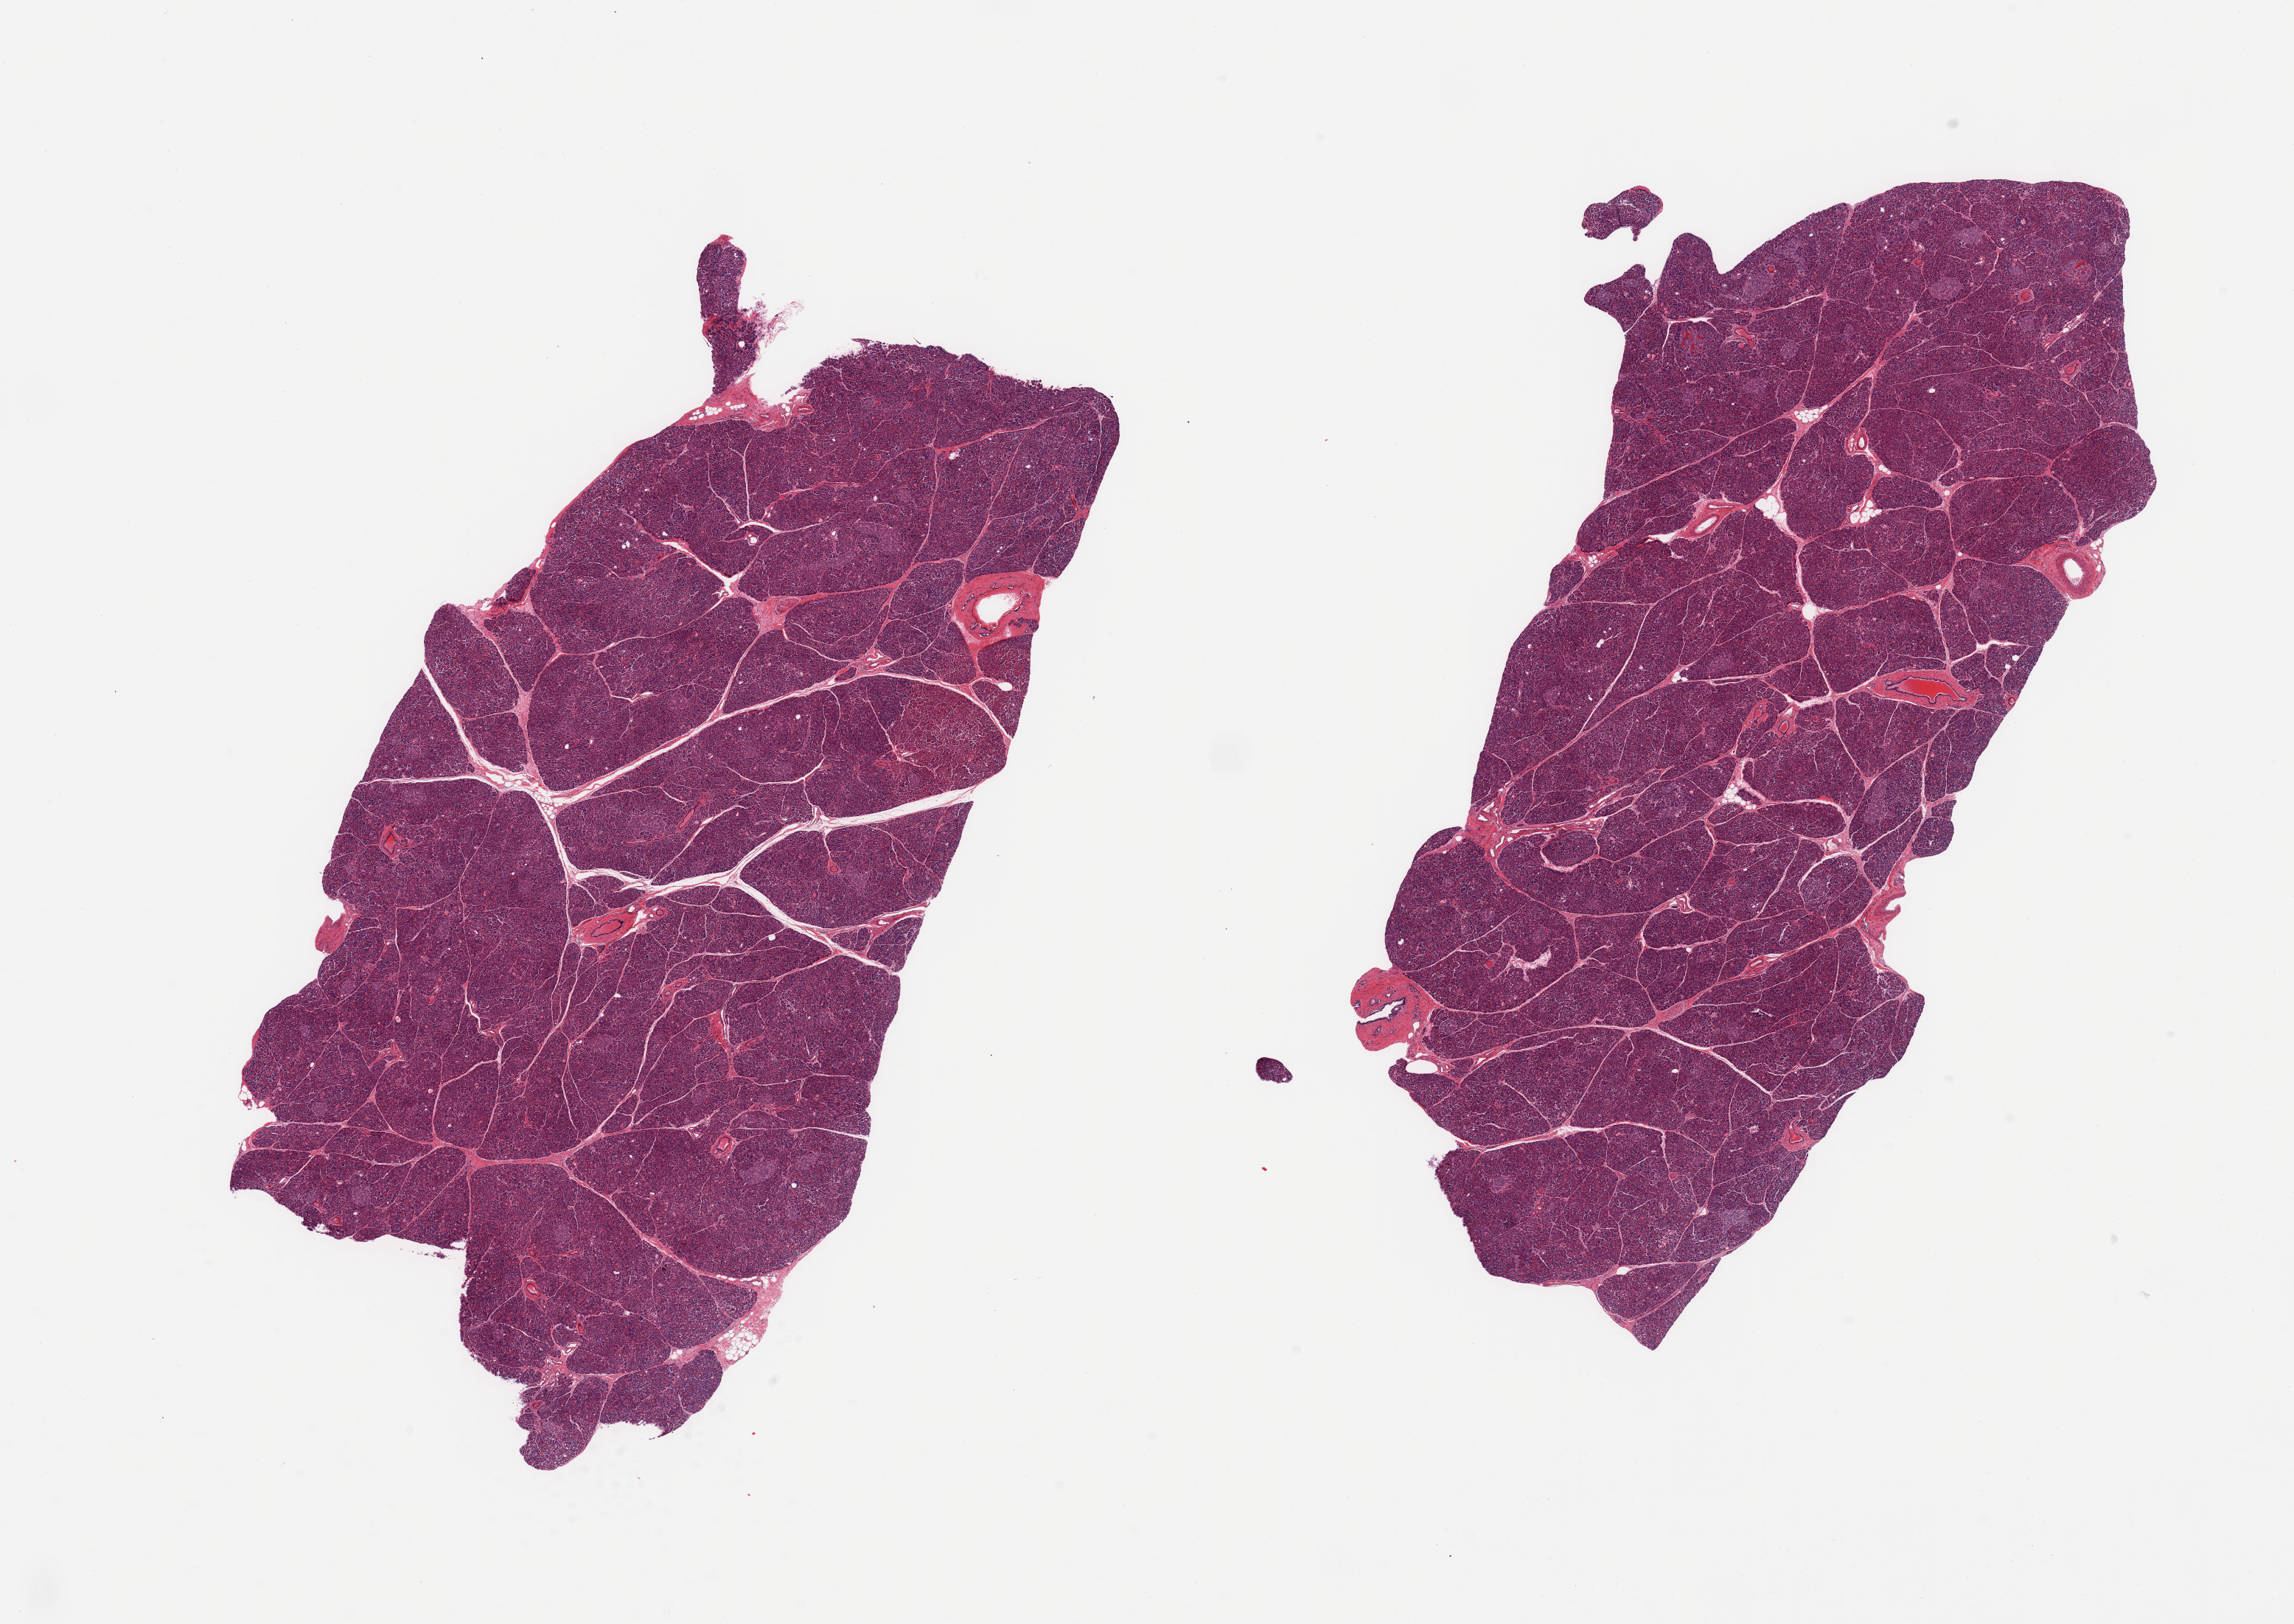
Digitized H&E-stained section, brightfield, a low-resolution overview of the entire scanned area, about 24.6 x 17.4 mm (slide scanned at 20x), PAXgene-fixed paraffin-embedded (PFPE) section, target tissue: pancreas, tissue donor sample. Donor sex: male.
Review note (as recorded): 2 pieces, well -preserved Islets present in rare numbers.